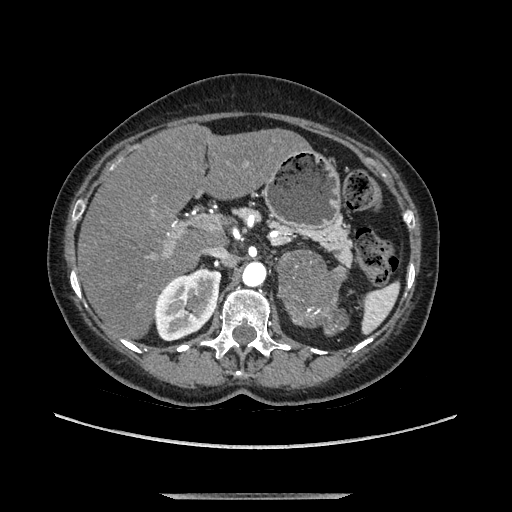
Contrast-enhanced abdominal CT, one axial slice. Slice 74 of 169 in the series (ordered by position). Soft-tissue window (W 400 / L 40 HU). 1.25 mm slice thickness. 512 × 512 image matrix, field of view 400 × 400 mm. Female patient. Case-level facts recorded for this patient, not image findings: diagnosis: adrenocortical carcinoma; tumour side: left adrenal; tumour size at pathology: 9 cm; Ki-67 index: 2 %; stage (as recorded): 3.
Annotated regions visible in this slice (semi-automatically segmented with operator editing):
- mass: bounding box <281,252,347,333> (left, top, right, bottom; pixels)